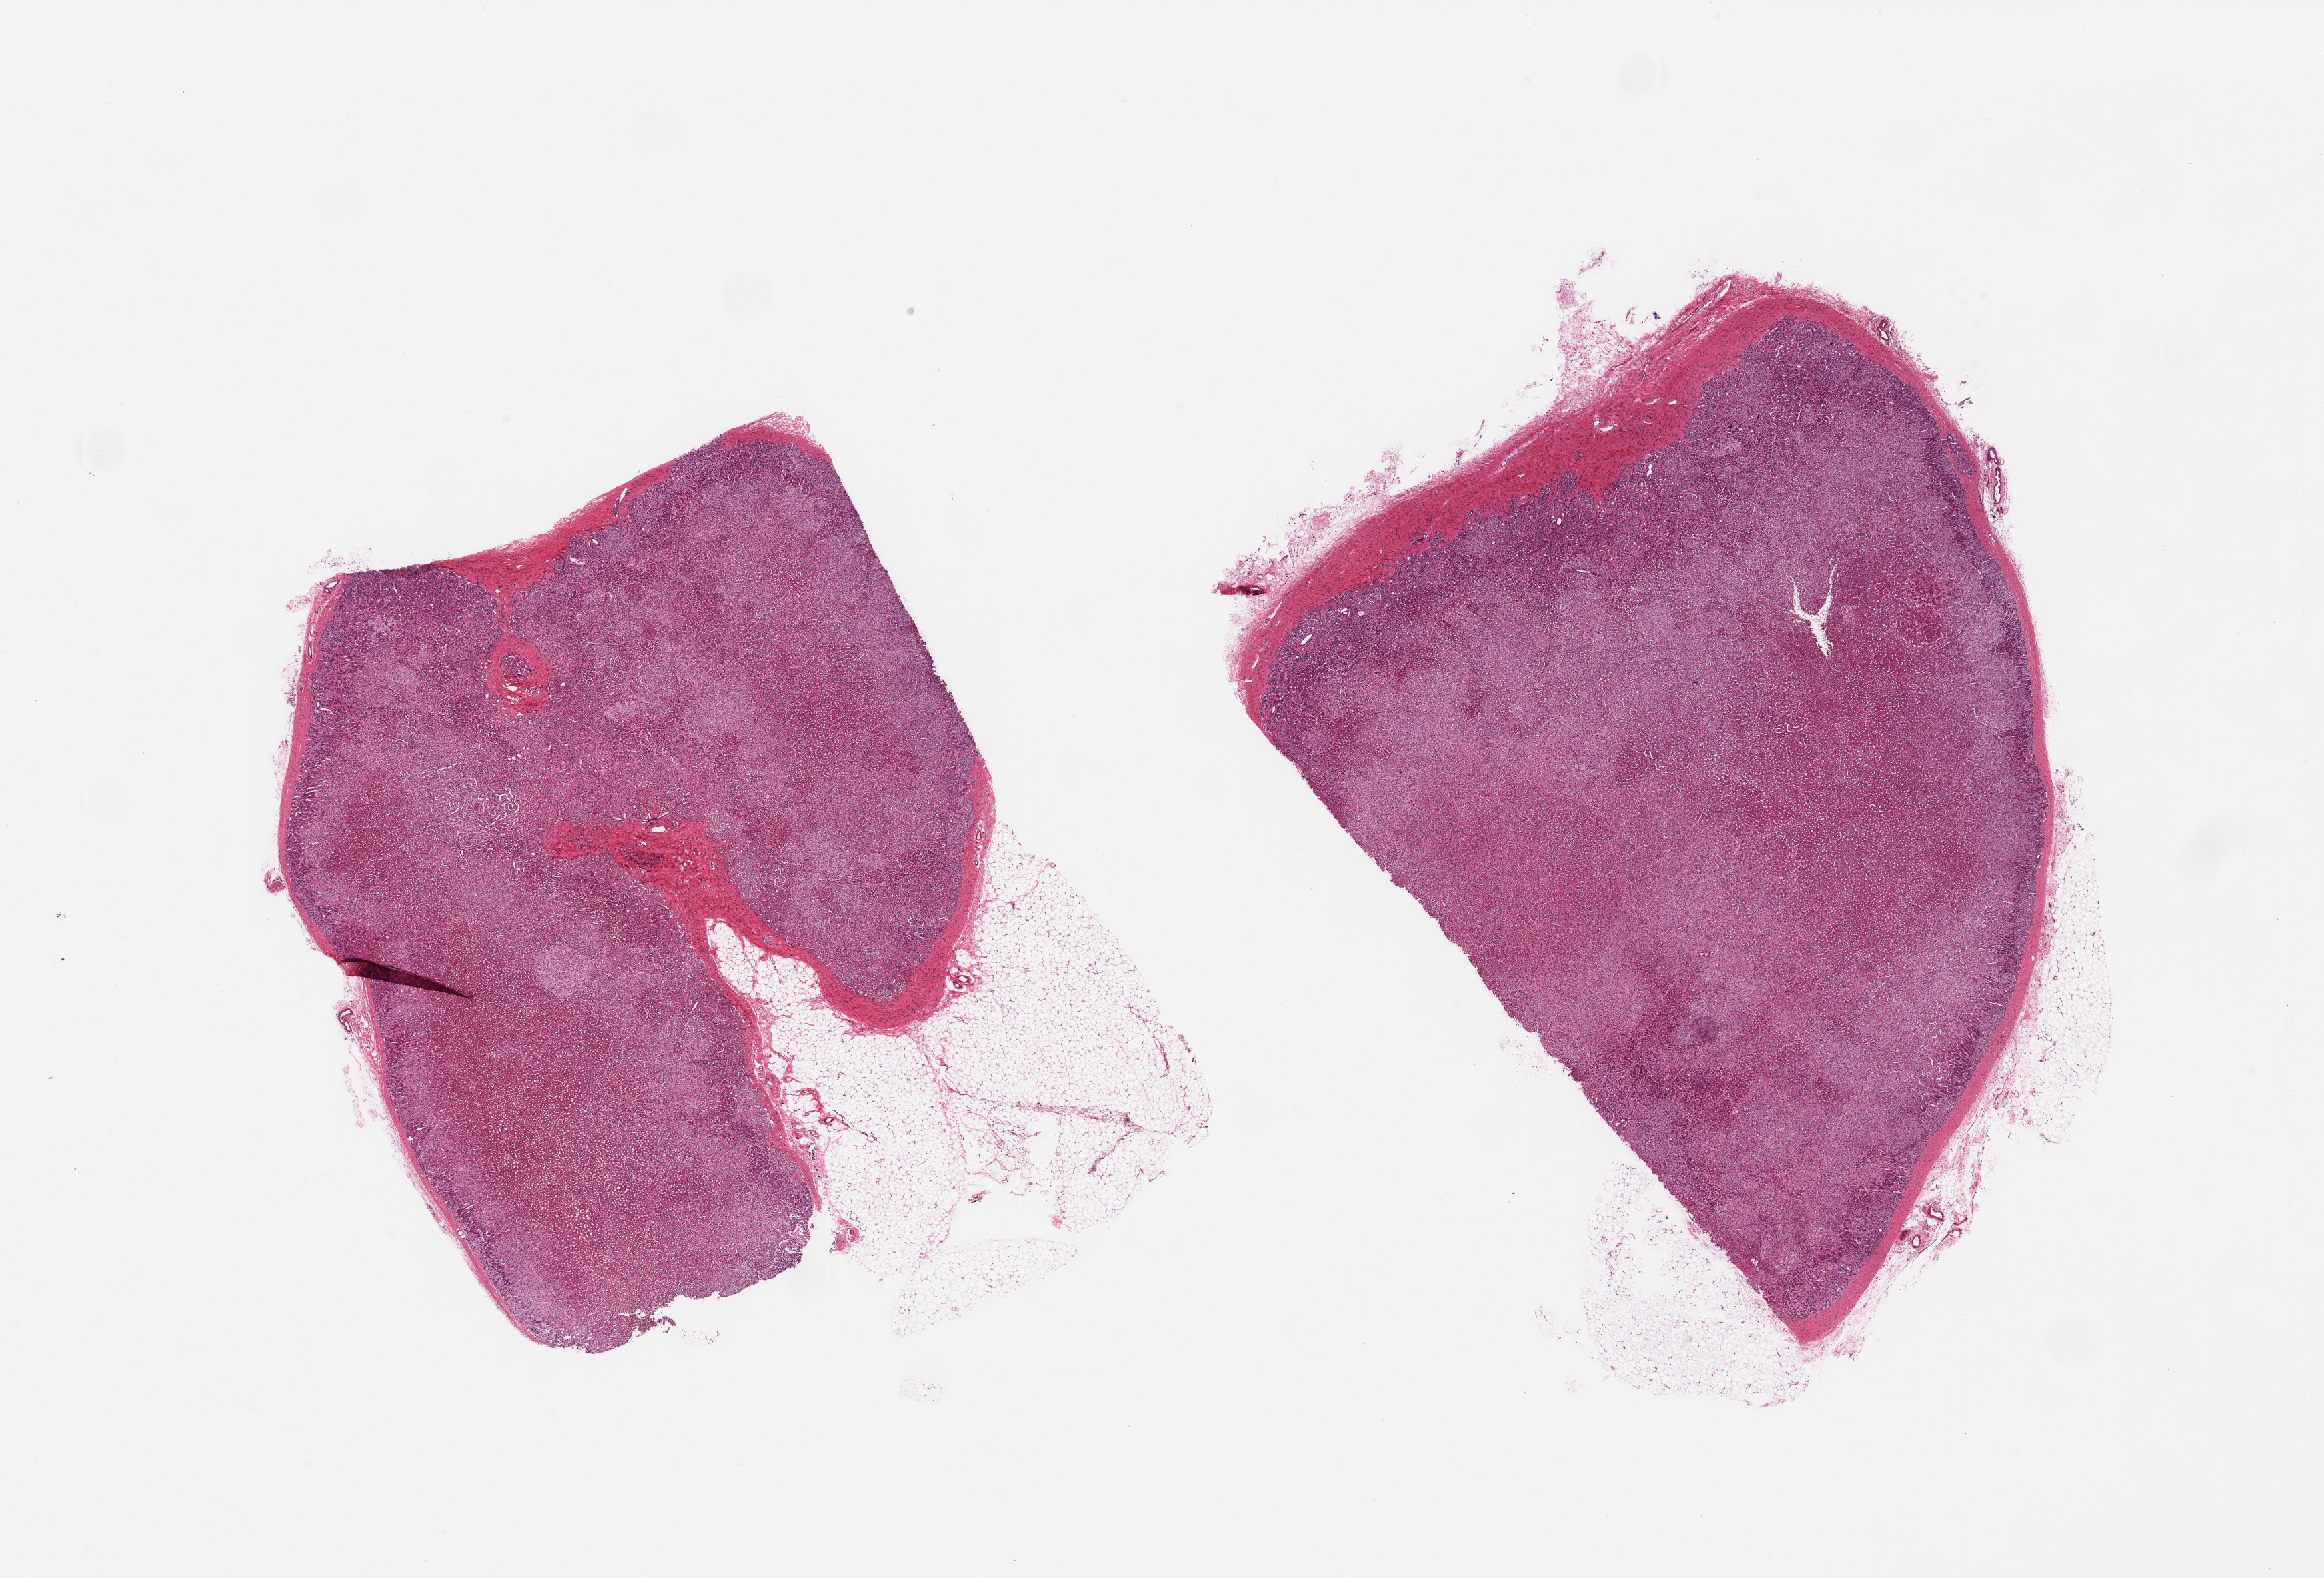
Hematoxylin and eosin (H&E) whole-slide image — a low-resolution overview of the entire scanned area, about 27.6 x 18.7 mm. PAXgene-fixed paraffin-embedded (PFPE) section. Sampled site (target tissue): adrenal gland. Donor tissue sample.
* review note (as recorded): 2 pieces, cortex, ~15% adherent fat